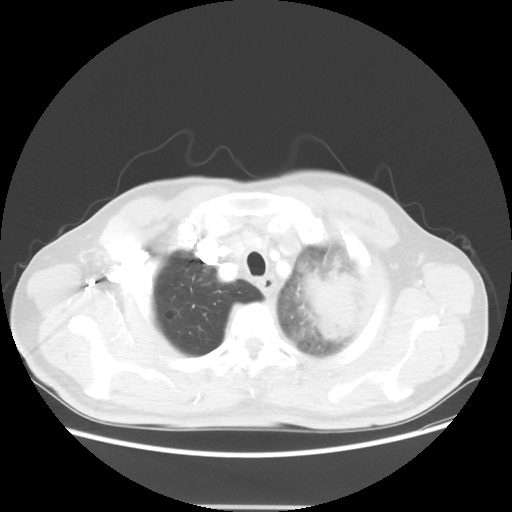
Chest CT, one axial slice. Slice 49 of 53 in the series (ordered by position). Reconstruction kernel STANDARD. 100 kVp. Lung window (W 1500 / L -600 HU). 5 mm slice thickness. 512 × 512 image matrix, field of view 391 × 391 mm. Patient: male, 60 years. Case-level facts recorded for this patient, not image findings: clinical TNM (as recorded): T4 N1 M1a; histopathological grade: G3.
Structures marked on this image (rectangle marked by the reading radiologist):
- lung tumour (recorded histology: large cell carcinoma): box from (x=295, y=257) to (x=364, y=345) px